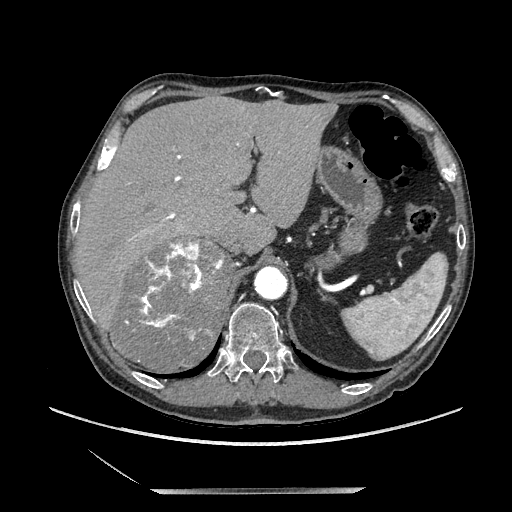
Contrast-enhanced abdominal CT, one axial slice; position 155 of 243 along the scan axis; soft-tissue window (W 400 / L 40 HU); 512 × 512 image matrix, field of view 420 × 420 mm. Male patient. Case-level facts recorded for this patient, not image findings: diagnosis: adrenocortical carcinoma; tumour side: right adrenal; tumour size at pathology: 16 cm; Ki-67 index: 17 %; stage (as recorded): 3.
Outlined on this slice (semi-automatically segmented with operator editing):
- mass: box from (x=115, y=238) to (x=231, y=372) px